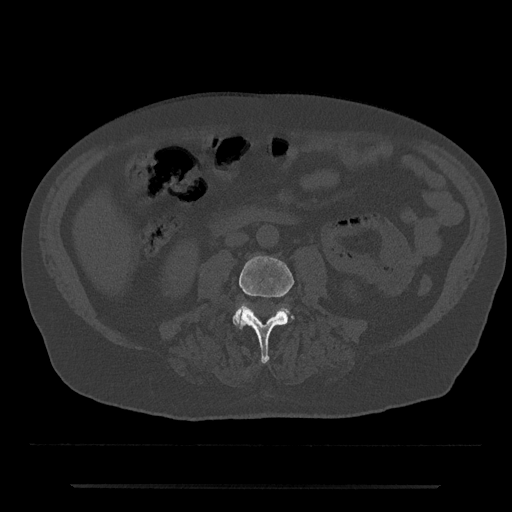
CT including the spine, one axial slice. Position 396 of 797 along the scan axis. 120 kVp. Bone window (W 1800 / L 400 HU). 0.5 mm slice thickness. 512 × 512 image matrix, field of view 434 × 434 mm. Male patient, age 80 years. Case-level facts recorded for this patient, not image findings: primary cancer: prostate; vertebrae with lytic lesions (as recorded): L1, T11.
Structures marked on this image (semi-automatically segmented with operator editing):
- L3 vertebra: bounding box <238,256,294,364> (left, top, right, bottom; pixels)
- L4 vertebra: <233,306,292,326>